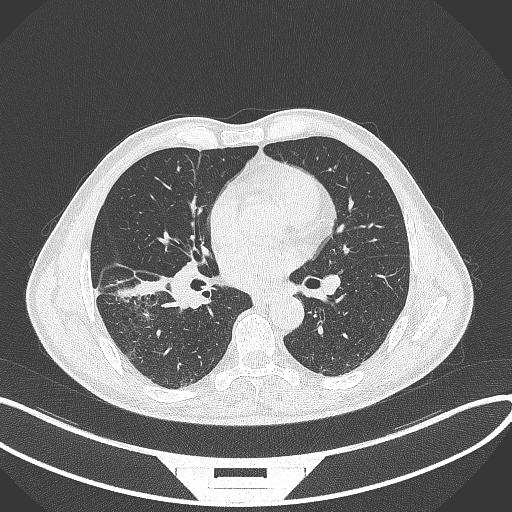
Chest CT, one axial slice. Position 174 of 364 along the scan axis. Reconstruction kernel B70f. 120 kVp. Lung window (W 1500 / L -600 HU). 1 mm slice thickness. 512 × 512 image matrix, field of view 400 × 400 mm. Male patient, age 58 years. From the clinical record (not read from this slice): clinical TNM (as recorded): T3 N0 M0; histopathological grade: G2.
Structures marked on this image (bounding box drawn by a radiologist):
- lung tumour (recorded histology: squamous cell carcinoma): bounding box [x1, y1, x2, y2] px = [117, 272, 171, 303]